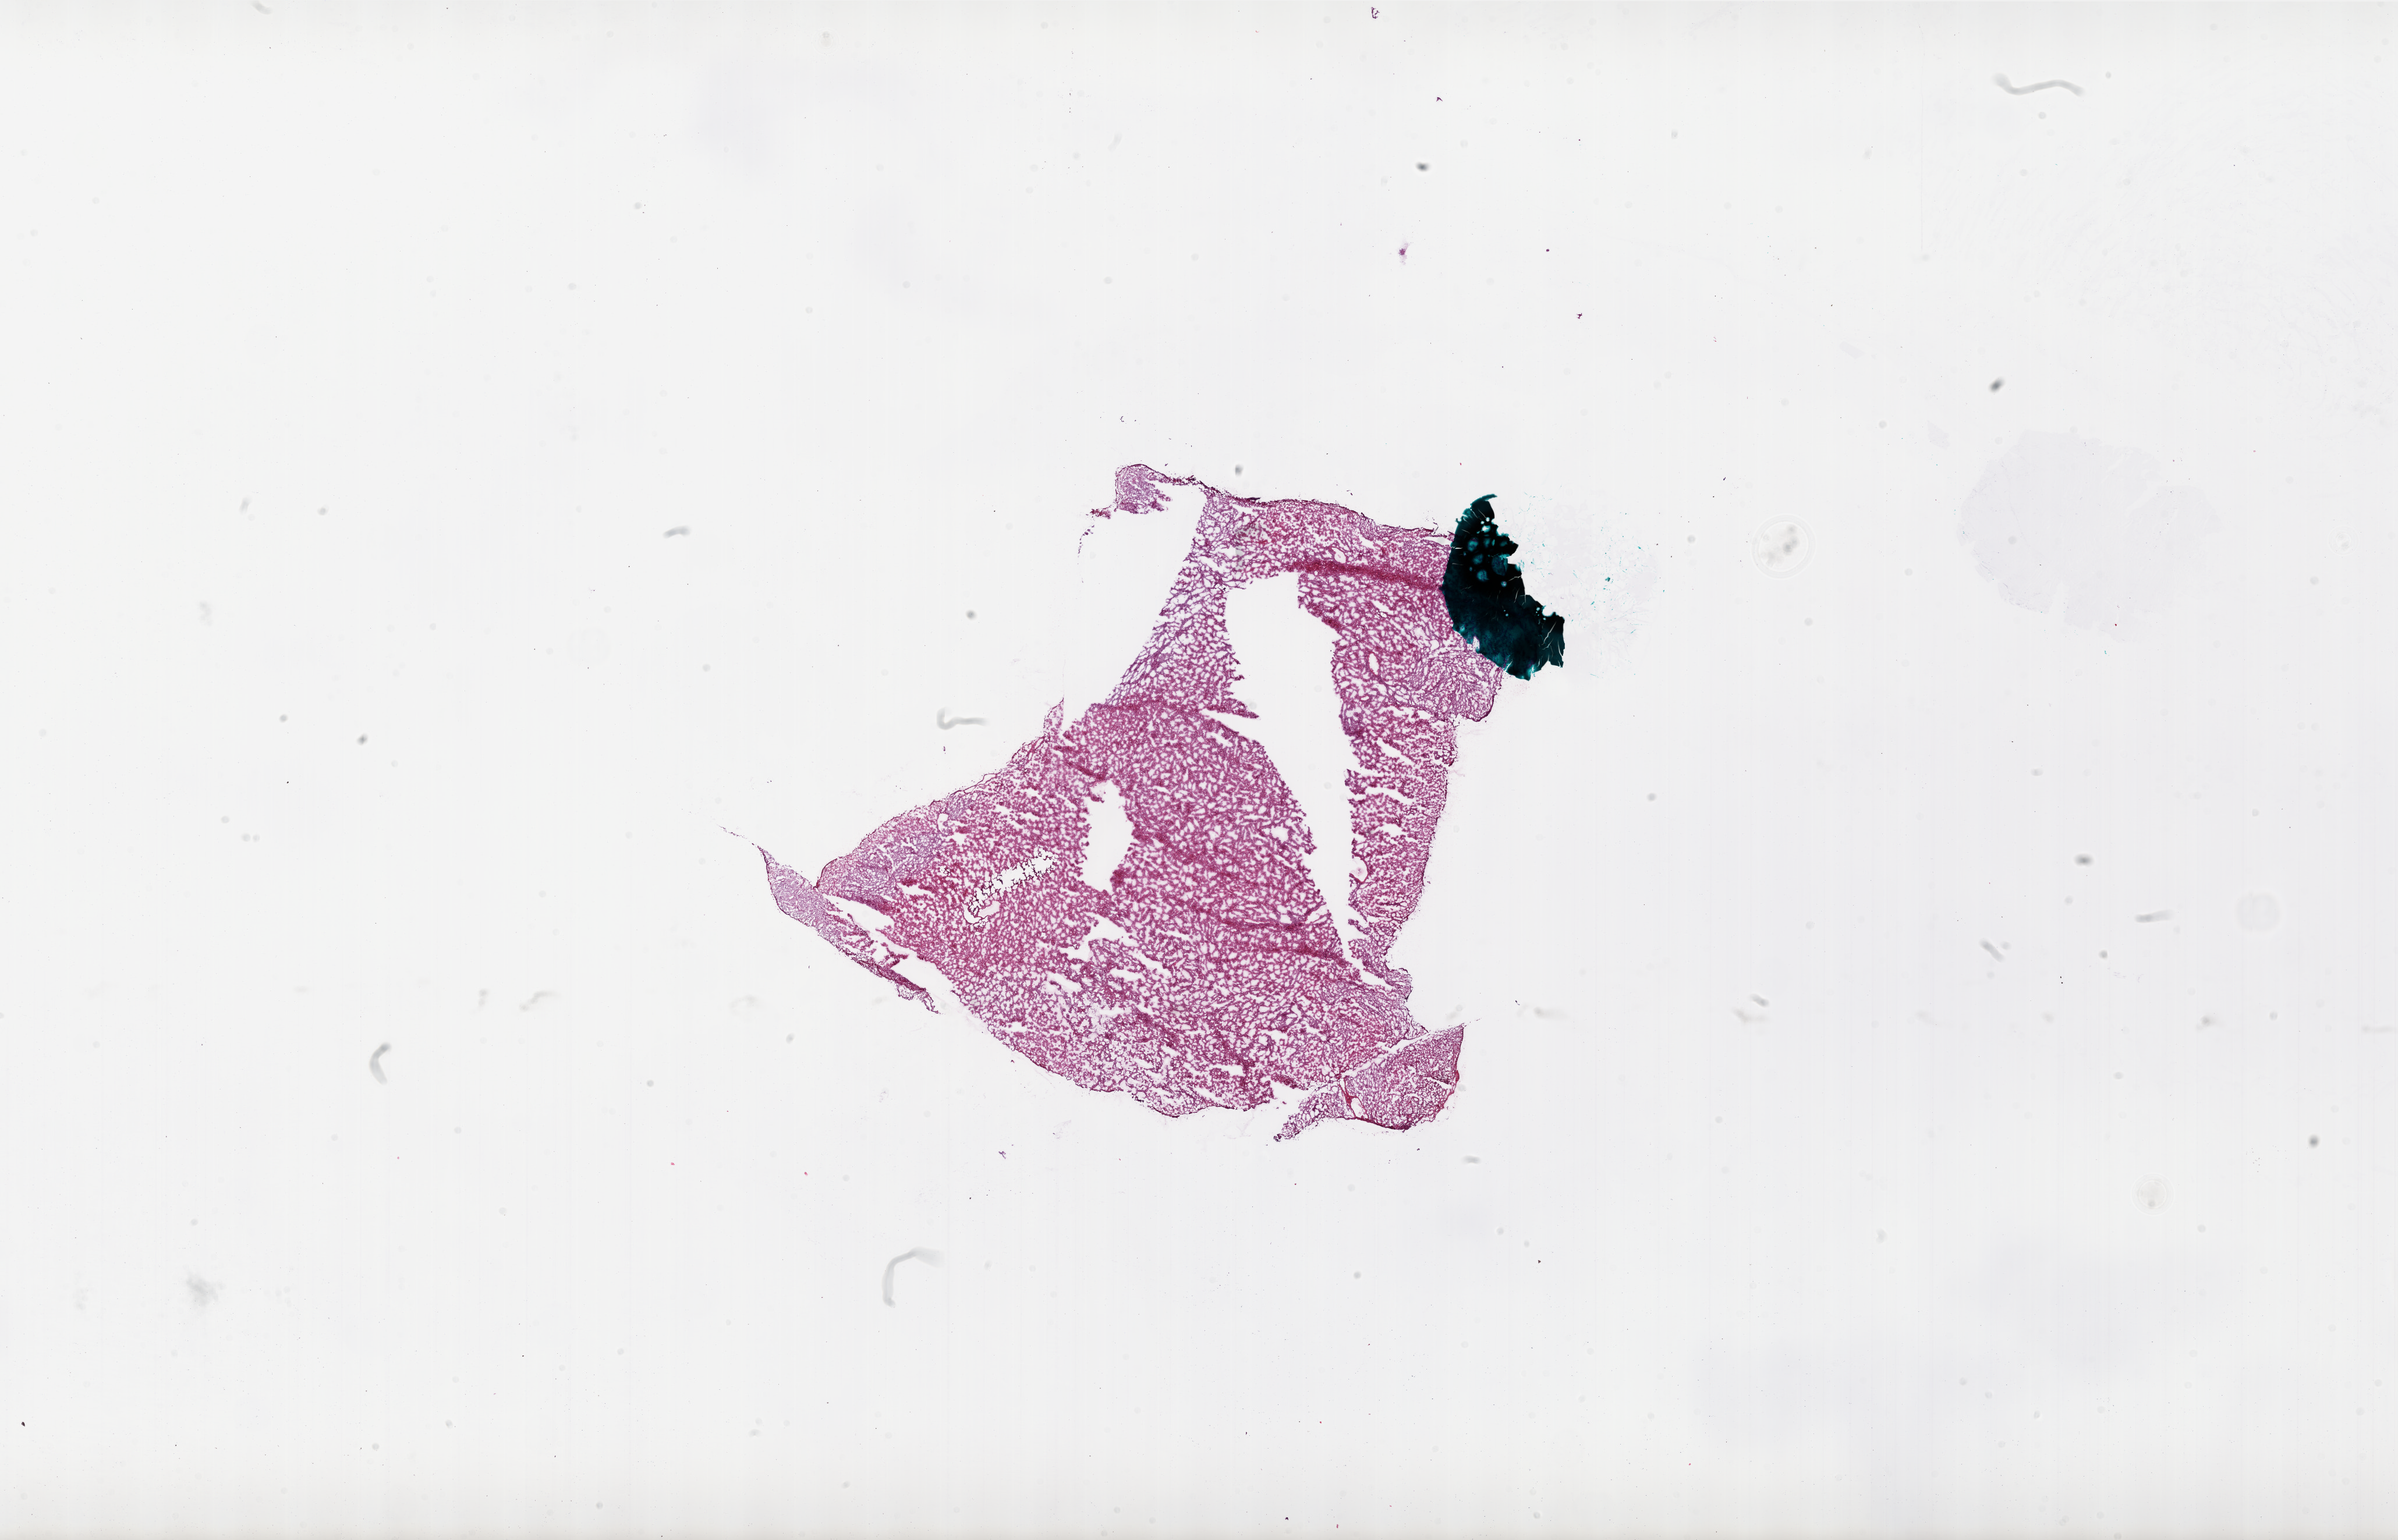
Digitized H&E tissue section (whole slide), a low-resolution overview of the entire scanned area, about 33.0 x 21.2 mm. Composition of this section per pathologist review: tumour cells 95%, tumour nuclei 80%, normal cells 0%, stromal cells 0%, necrosis 5%.
Specimen: frozen section; brain, primary tumour sample.